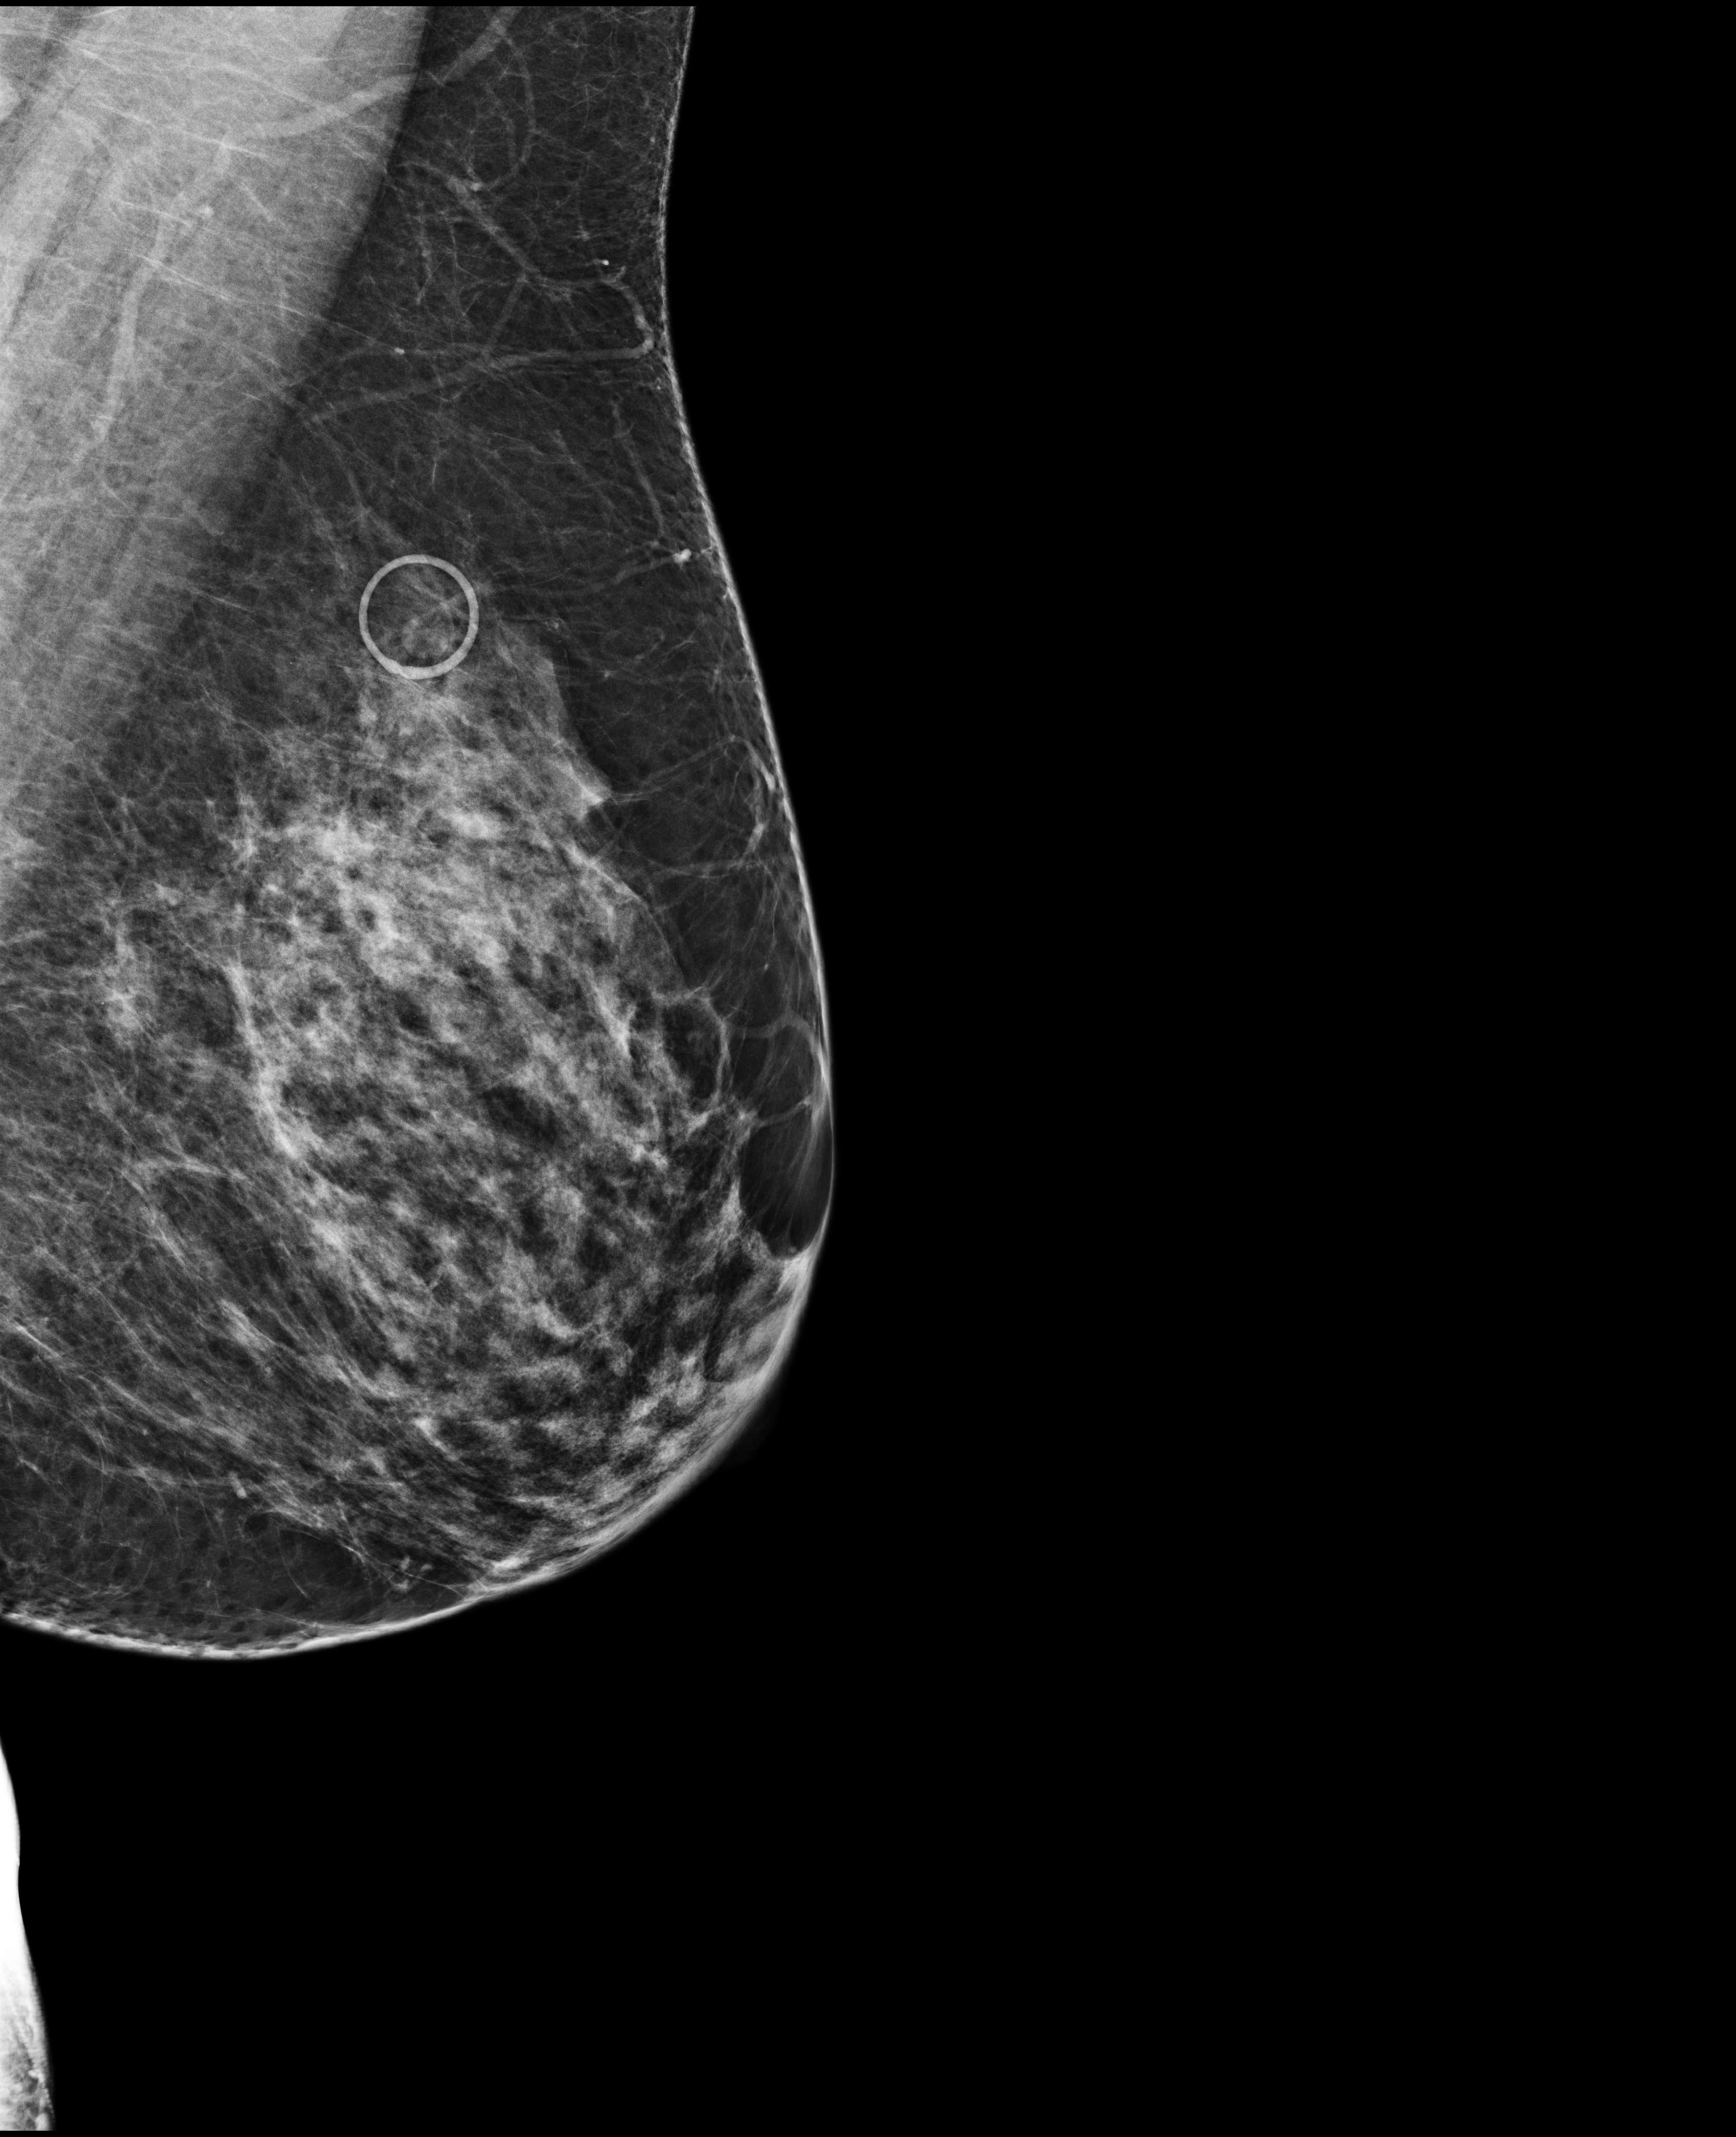
Annual screening mammography examination. Patient aged 53 years (female).
Image type: full-field digital mammogram. Breast: left. Projection: mediolateral oblique (MLO) view.